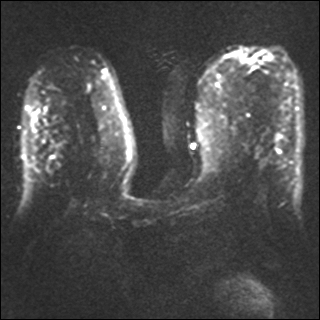
Breast MRI, one axial slice. Slice 17 of 40 in the series (ordered by position). Diffusion-weighted series; image 2 of 4 stored at this slice position (different b-values; order by instance number). 1.5 T. 4 mm slice thickness. 320 × 320 image matrix, field of view 330 × 330 mm. Female patient.
Annotated regions visible in this slice (manually delineated by an expert):
- tumour on diffusion-weighted imaging: bounding box (x1, y1, x2, y2) in pixels: (252, 58, 257, 63)